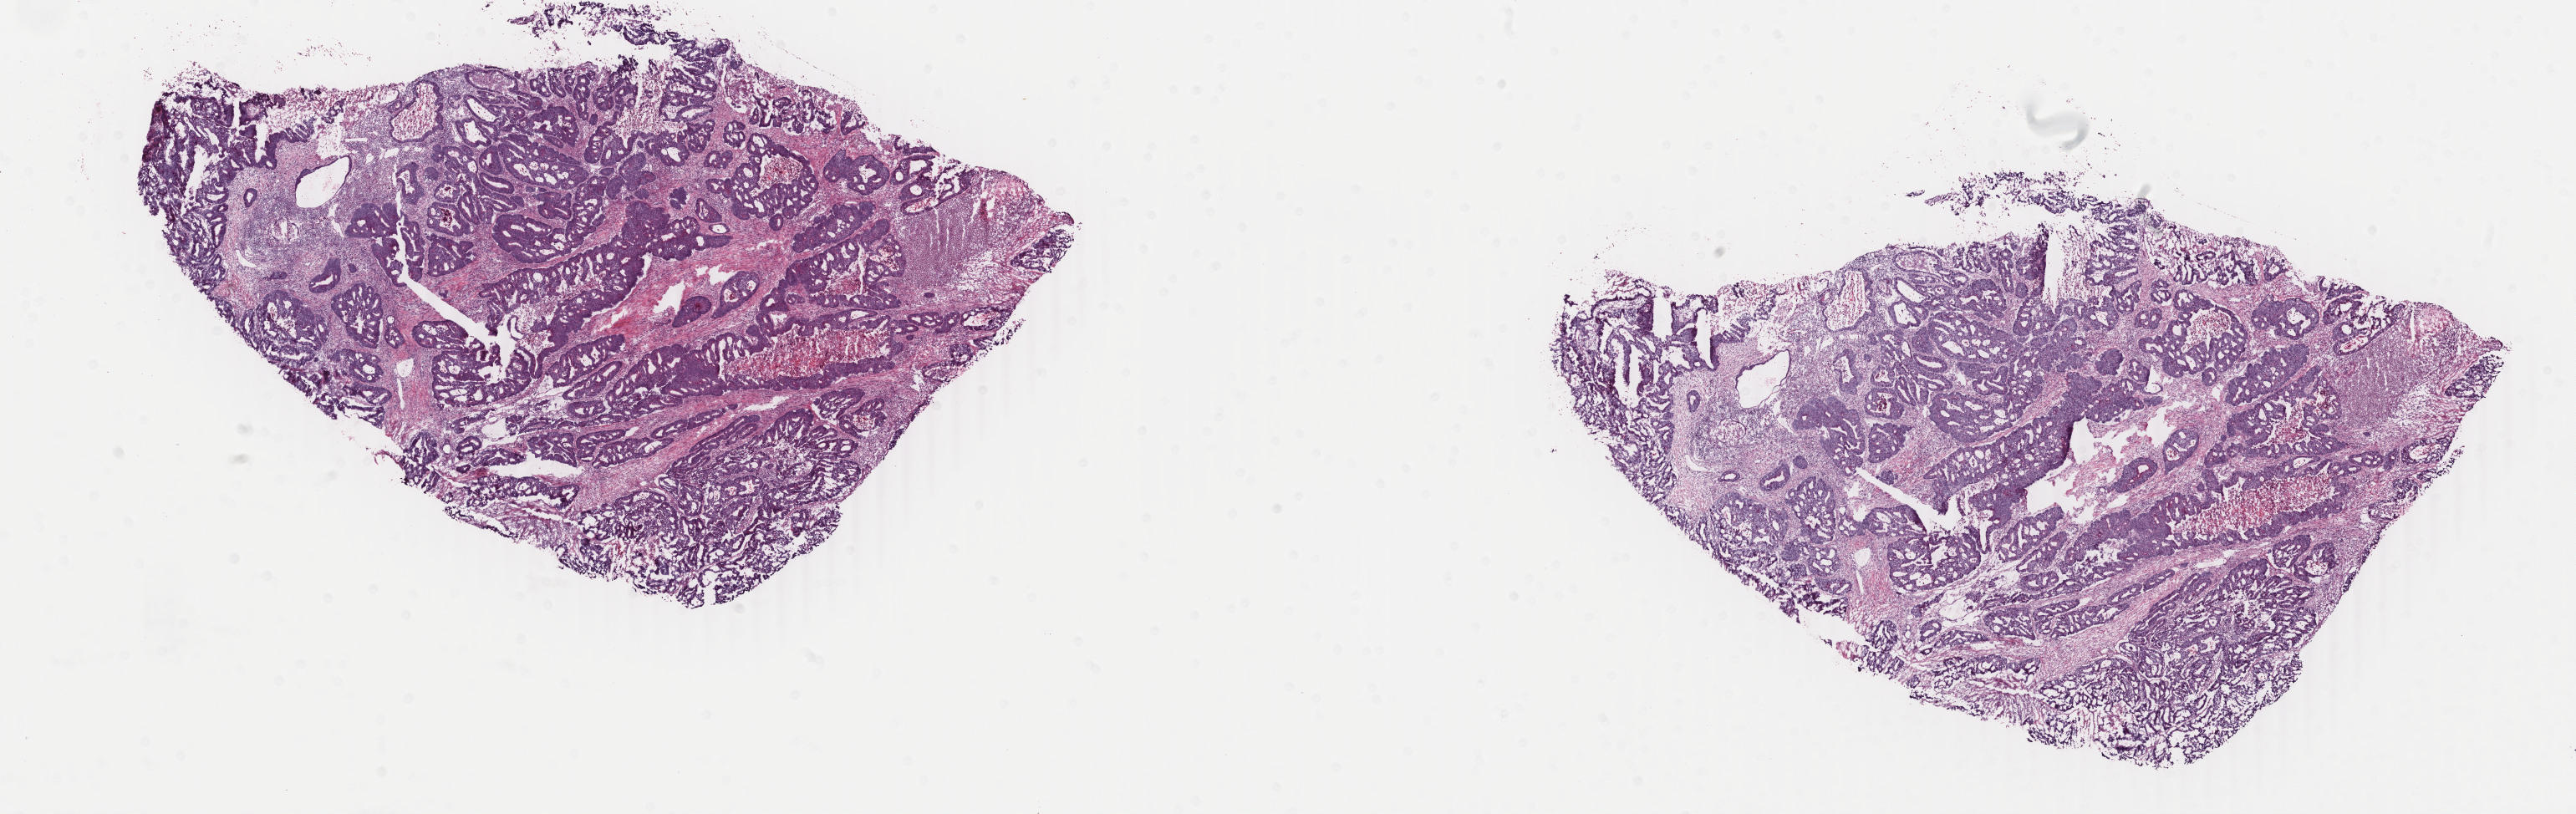
H&E-stained whole-slide image — shown as a low-resolution overview of the whole scanned area (about 24.5 x 7.7 mm, from a 40x scan), frozen section, primary tumour sample from the rectum. Female patient; age at initial diagnosis 57 years. Slide review estimates, as recorded: tumour cells 85%, tumour nuclei 85%, normal cells 0%, stromal cells 0%, necrosis 15%. Infiltration values recorded for this section: lymphocyte infiltration 0%, monocyte infiltration 0%, neutrophil infiltration 0%.
AJCC pathologic stage: IIA. Lymph nodes positive (case pathology): 0 of 14 examined. Pathologic diagnosis: Adenocarcinoma, NOS (rectosigmoid junction).